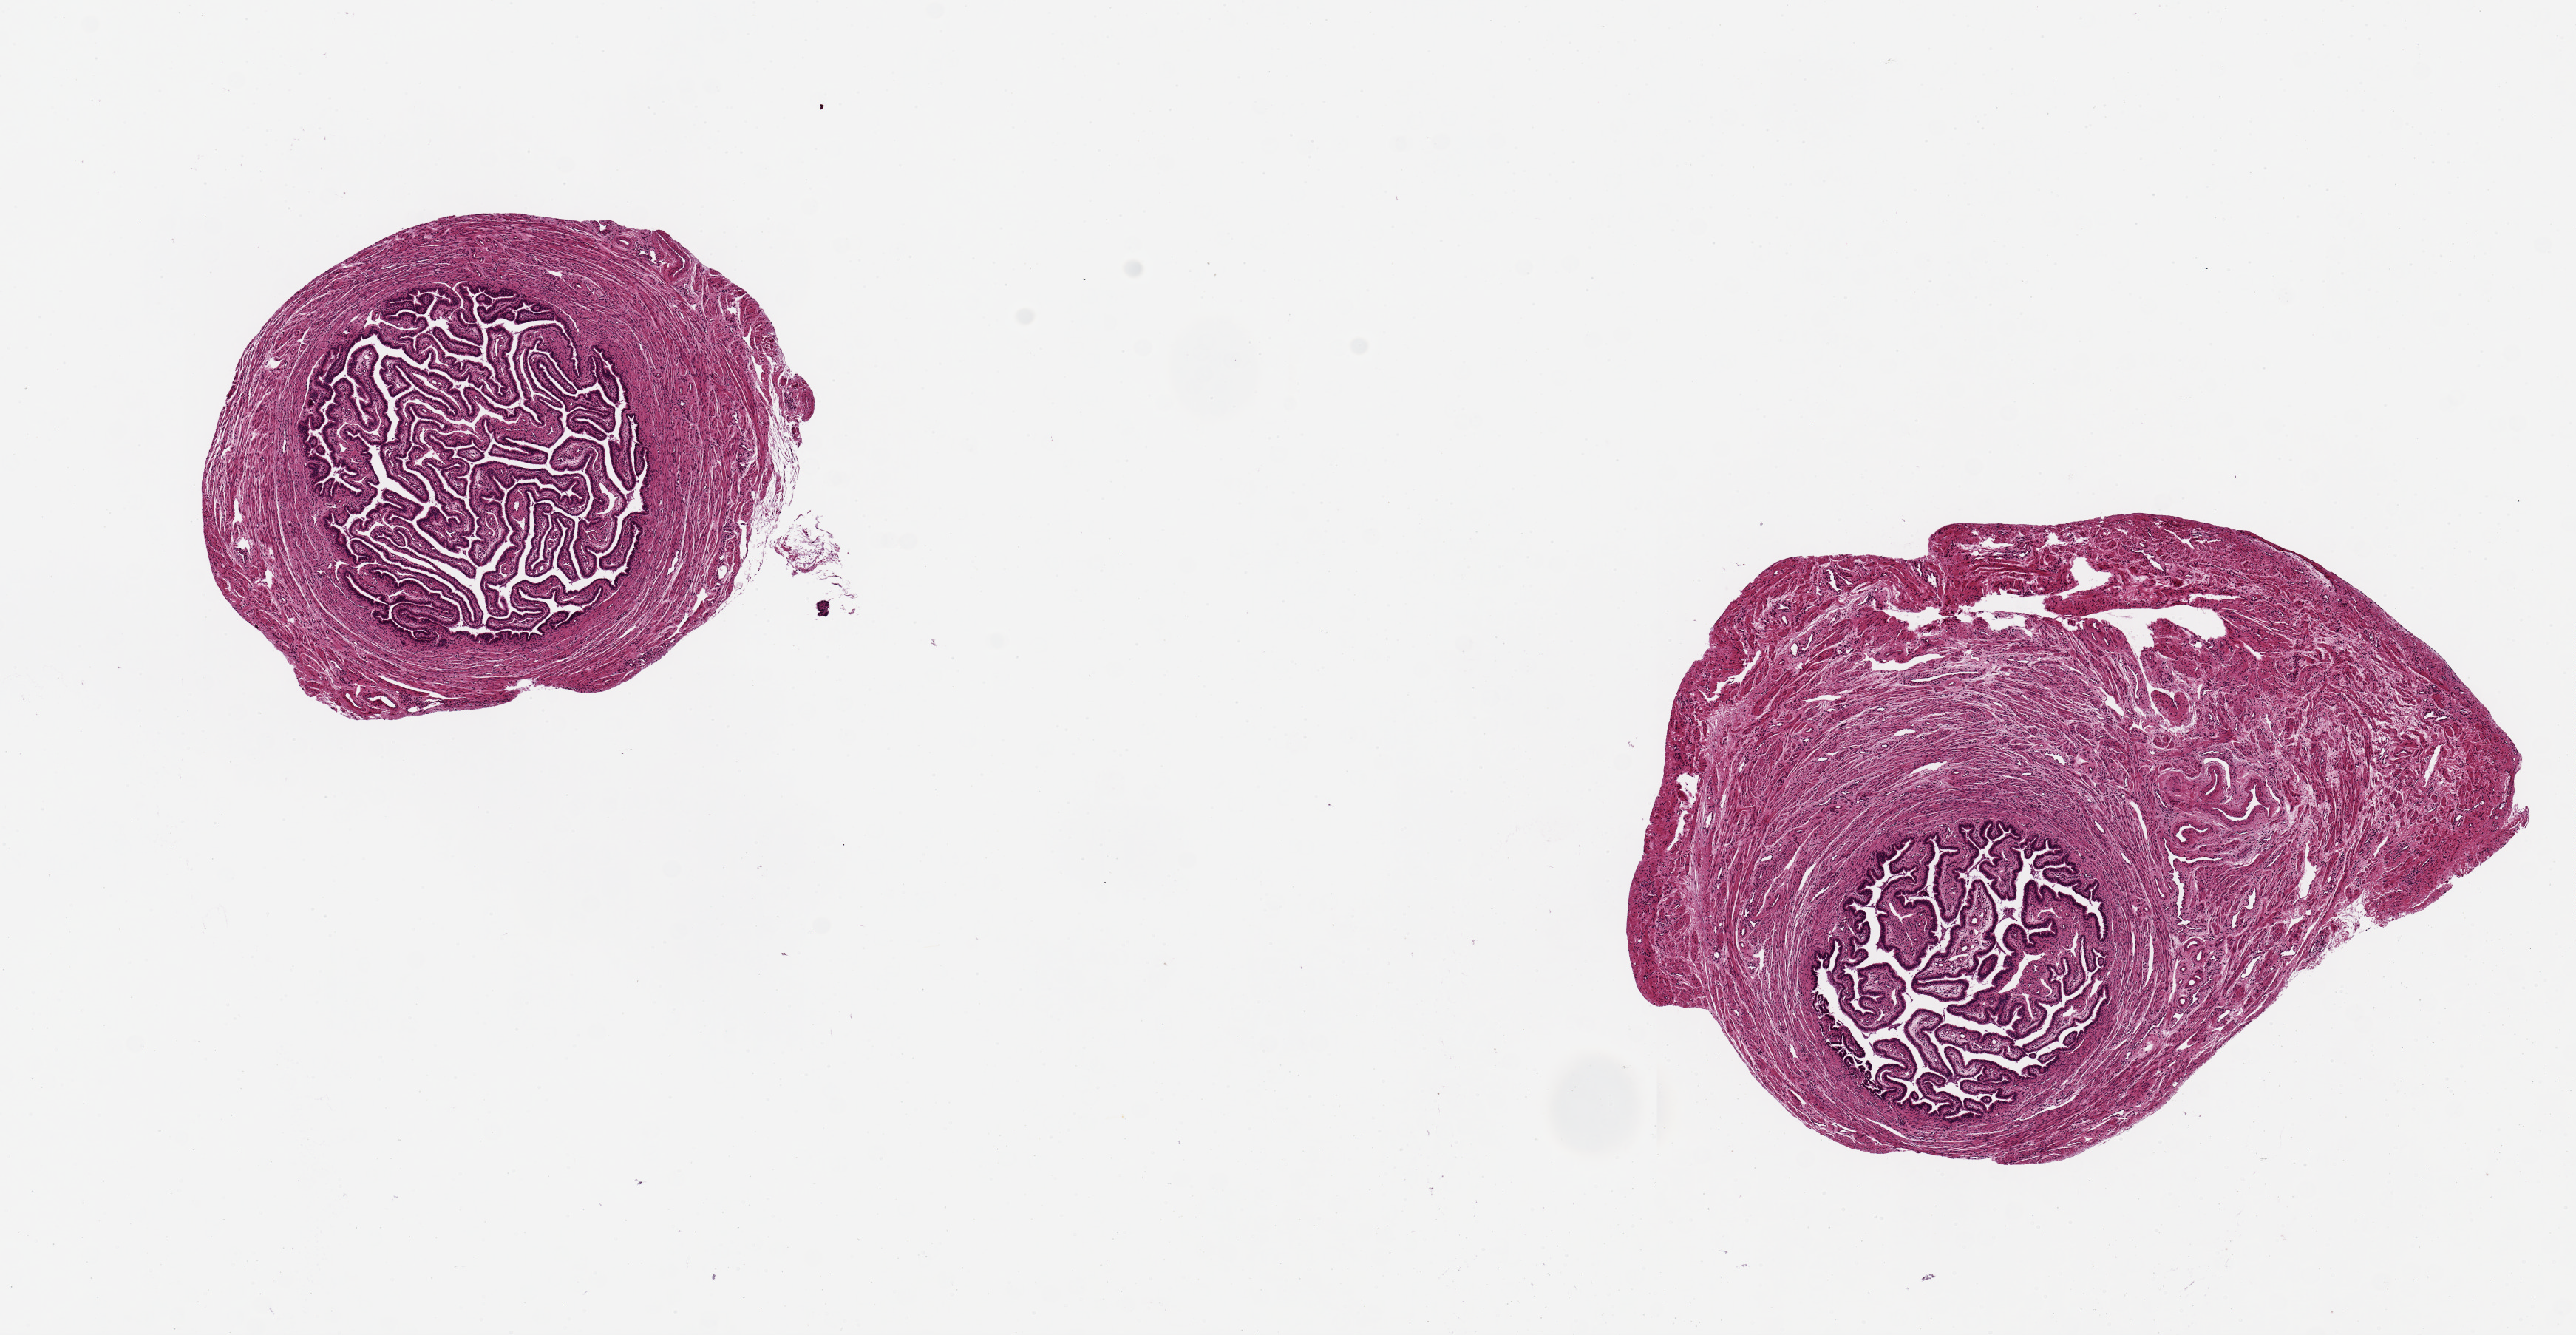
Whole-slide image, H&E stain, a low-resolution overview of the entire scanned area, about 13.8 x 7.1 mm; PAXgene-fixed, paraffin-embedded tissue; section of fallopian tube (target tissue); donor tissue sample. Donor: female.
Reviewer comment on this tissue sample: 2 pieces fallopian tube not ovary, may be used once label corrected.